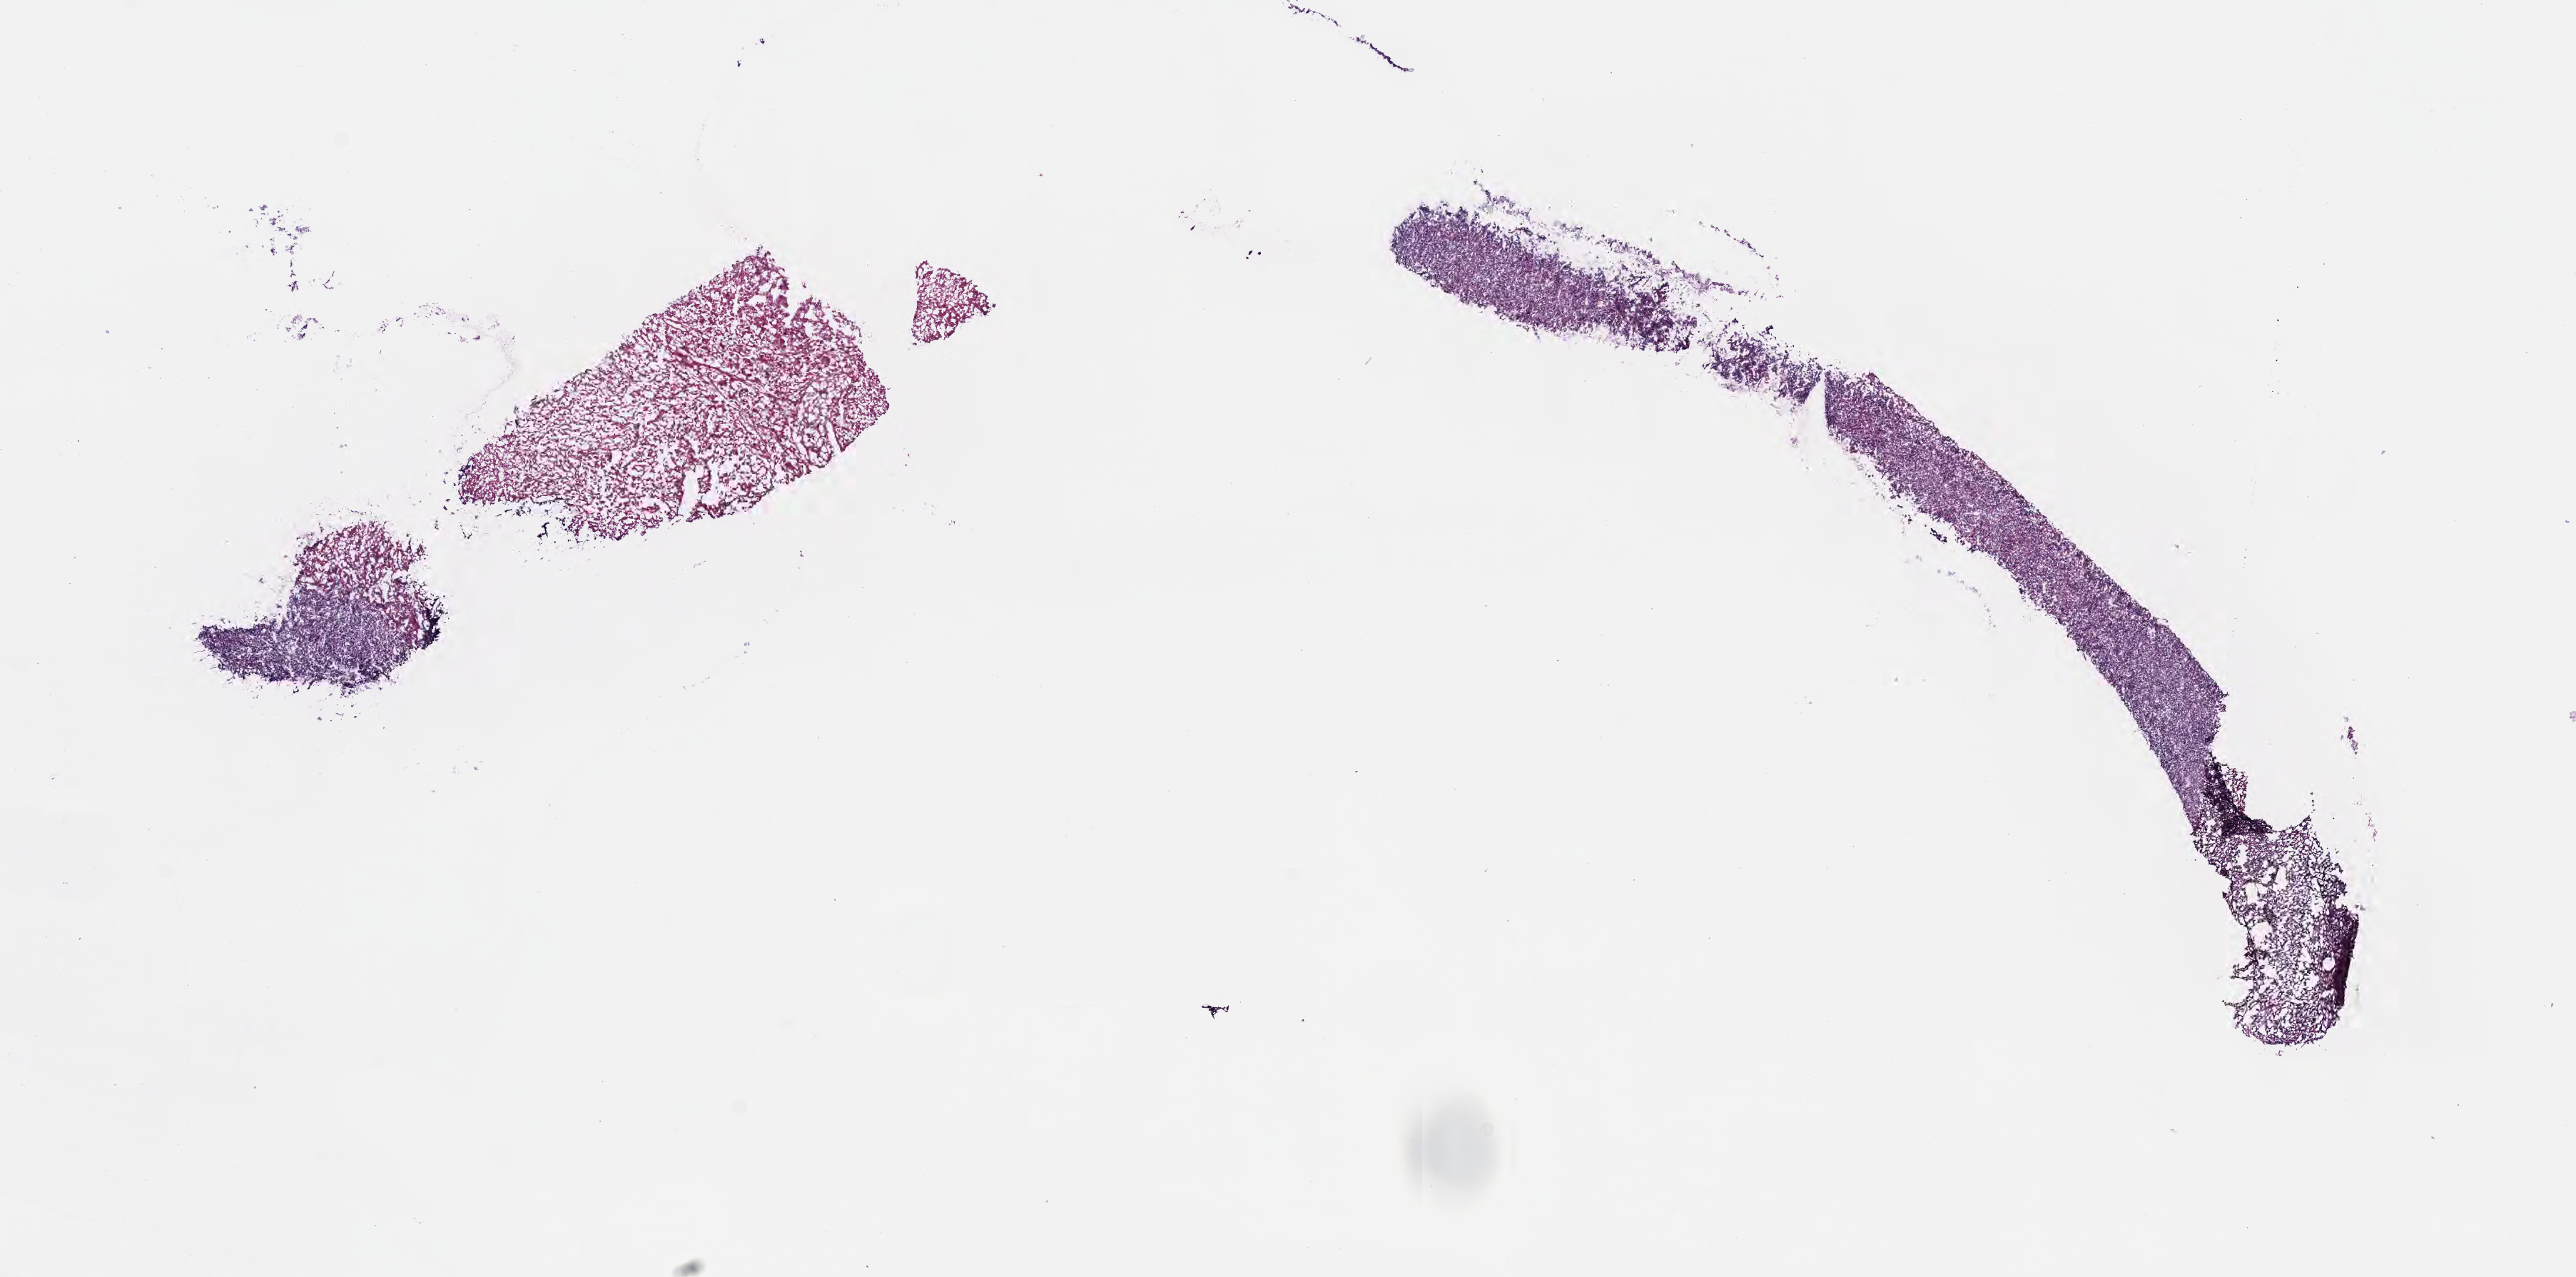
Hematoxylin and eosin (H&E) whole-slide image, shown as a low-resolution overview of the whole scanned area (about 14.6 x 7.2 mm); frozen section (tissue freezing medium); primary tumor; anatomic site: abdomen proper. Patient: male, aged 14. Pathologist review of this section (percent, as recorded): tumor cells 50%, tumor nuclei 90%, stromal cells 10%, necrosis 40%, normal cells 0%. Inflammatory infiltration, as recorded: lymphocyte infiltration 15%, monocyte infiltration 30%, neutrophil infiltration 15%.
Histologic diagnosis: Burkitt lymphoma, NOS. Section: top of the tissue portion. Ann Arbor stage (patient): Stage III.